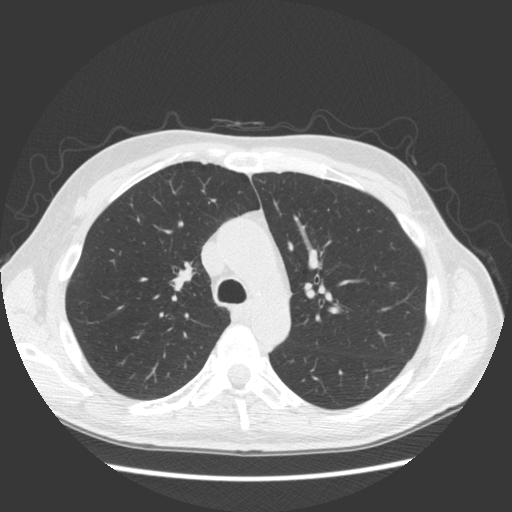
Axial slice from a low-dose chest CT screening exam, second annual screen, lung window (W 1500 / L -600 HU), 2.5 mm slice thickness, standard (soft-tissue) reconstruction kernel (STANDARD), slice 56 of 163 in the series, 512 × 512 image matrix, field of view 360 × 360 mm. Male, age 57 years at enrolment. Former smoker at enrolment.
Expert-annotated lung lesion, bounding box <153,250,204,300> (left, top, right, bottom; pixels). The screening reader recorded 3 non-calcified nodules or masses ≥4 mm on this exam (right middle lobe, right middle lobe, right middle lobe); which of them this box marks is not recorded. Later outcome: lung cancer diagnosed 264 days after this screen — adenocarcinoma, NOS, right upper lobe, poorly differentiated (G3), stage IB (AJCC 6th edition), 25 mm at pathology.